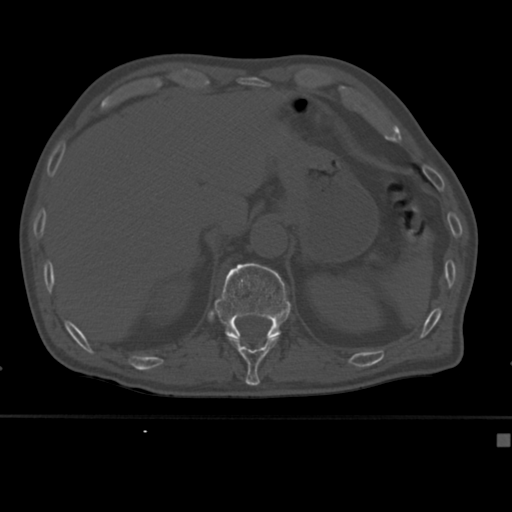
CT including the spine, one axial slice. Position 199 of 430 along the scan axis. Reconstruction kernel Br40s. Bone window (W 1800 / L 400 HU). 512 × 512 image matrix, field of view 337 × 337 mm. Male patient, age 64 years. Case-level facts recorded for this patient, not image findings: primary cancer: uterus.
Structures marked on this image (semi-automatically segmented with operator editing):
- T11 vertebra: bounding box [x1, y1, x2, y2] px = [228, 336, 278, 382]
- T12 vertebra: [214, 263, 291, 342]